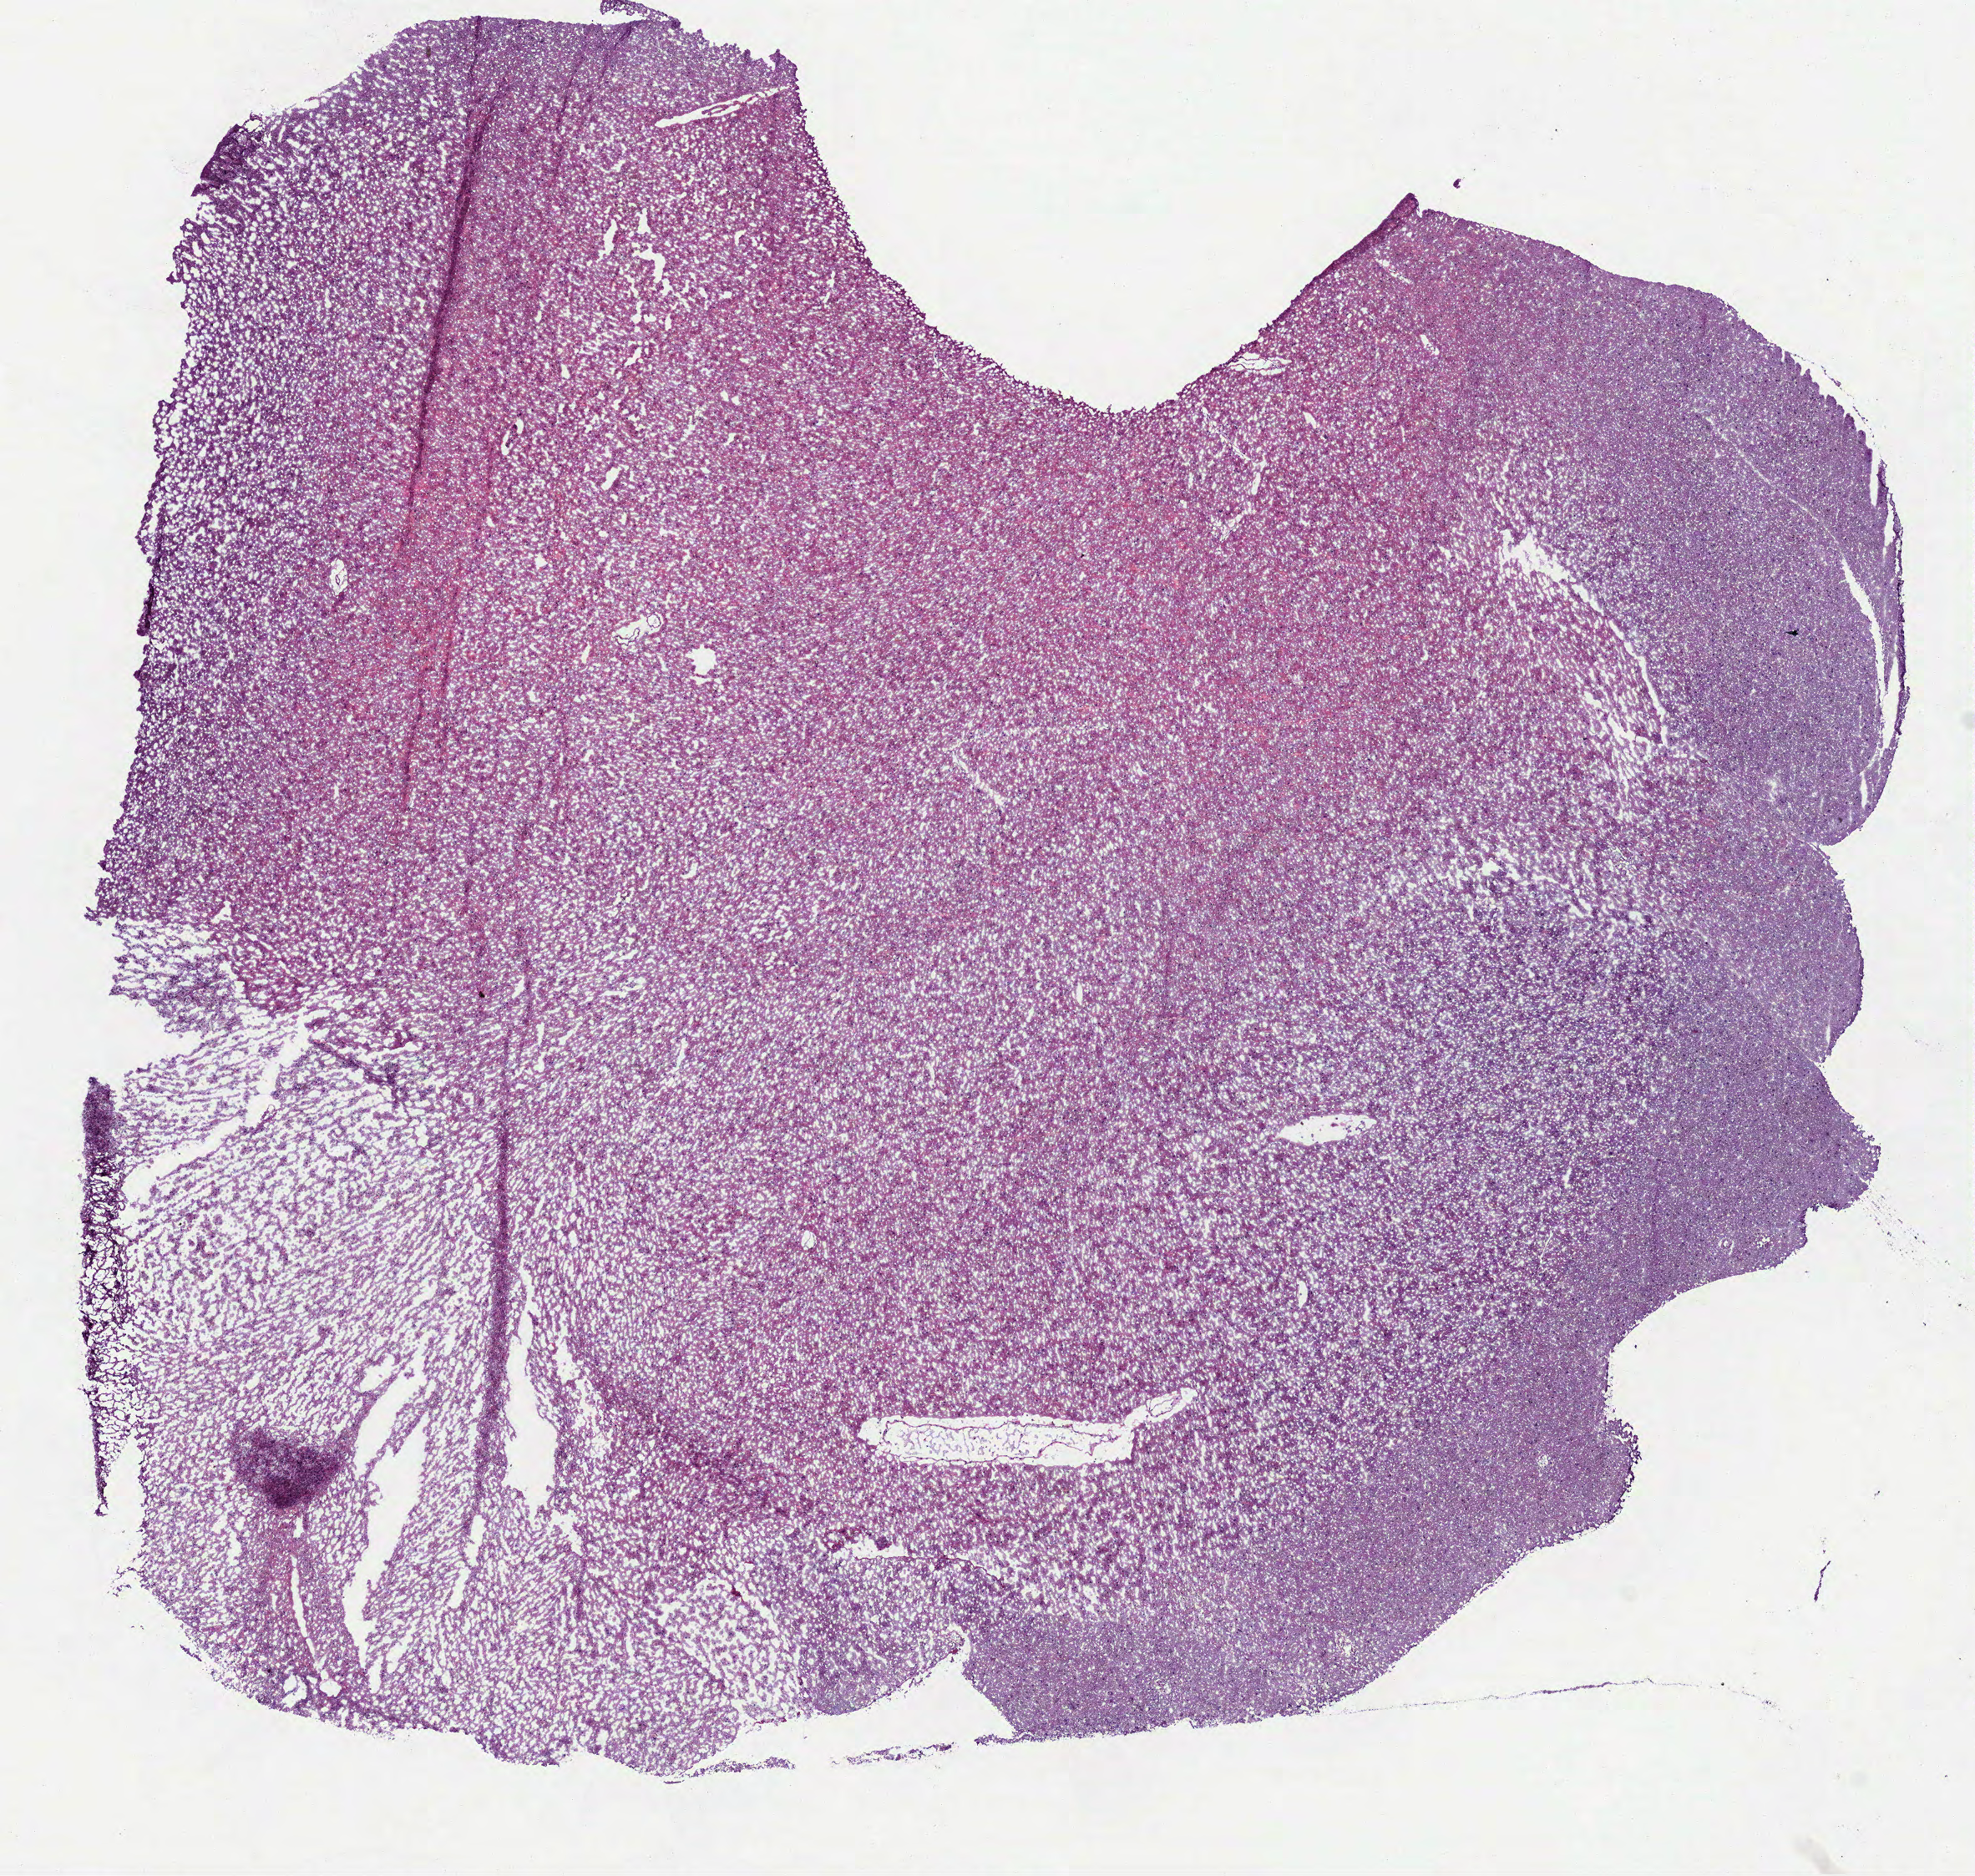
Whole-slide histology image, H&E — whole scanned area (about 9.5 x 9.1 mm, slide scanned at 40x) shown as a low-resolution overview, frozen section from the bottom of the tissue portion, primary tumour sample from the brain. Male, age 30 years at initial diagnosis. Histologic grade: G2 (moderately differentiated). Pathologist review of this section (percent, as recorded): tumour cells 100%, tumour nuclei 68%, normal cells 0%, stromal cells 0%, necrosis 0%.
Diagnosis: Mixed glioma.